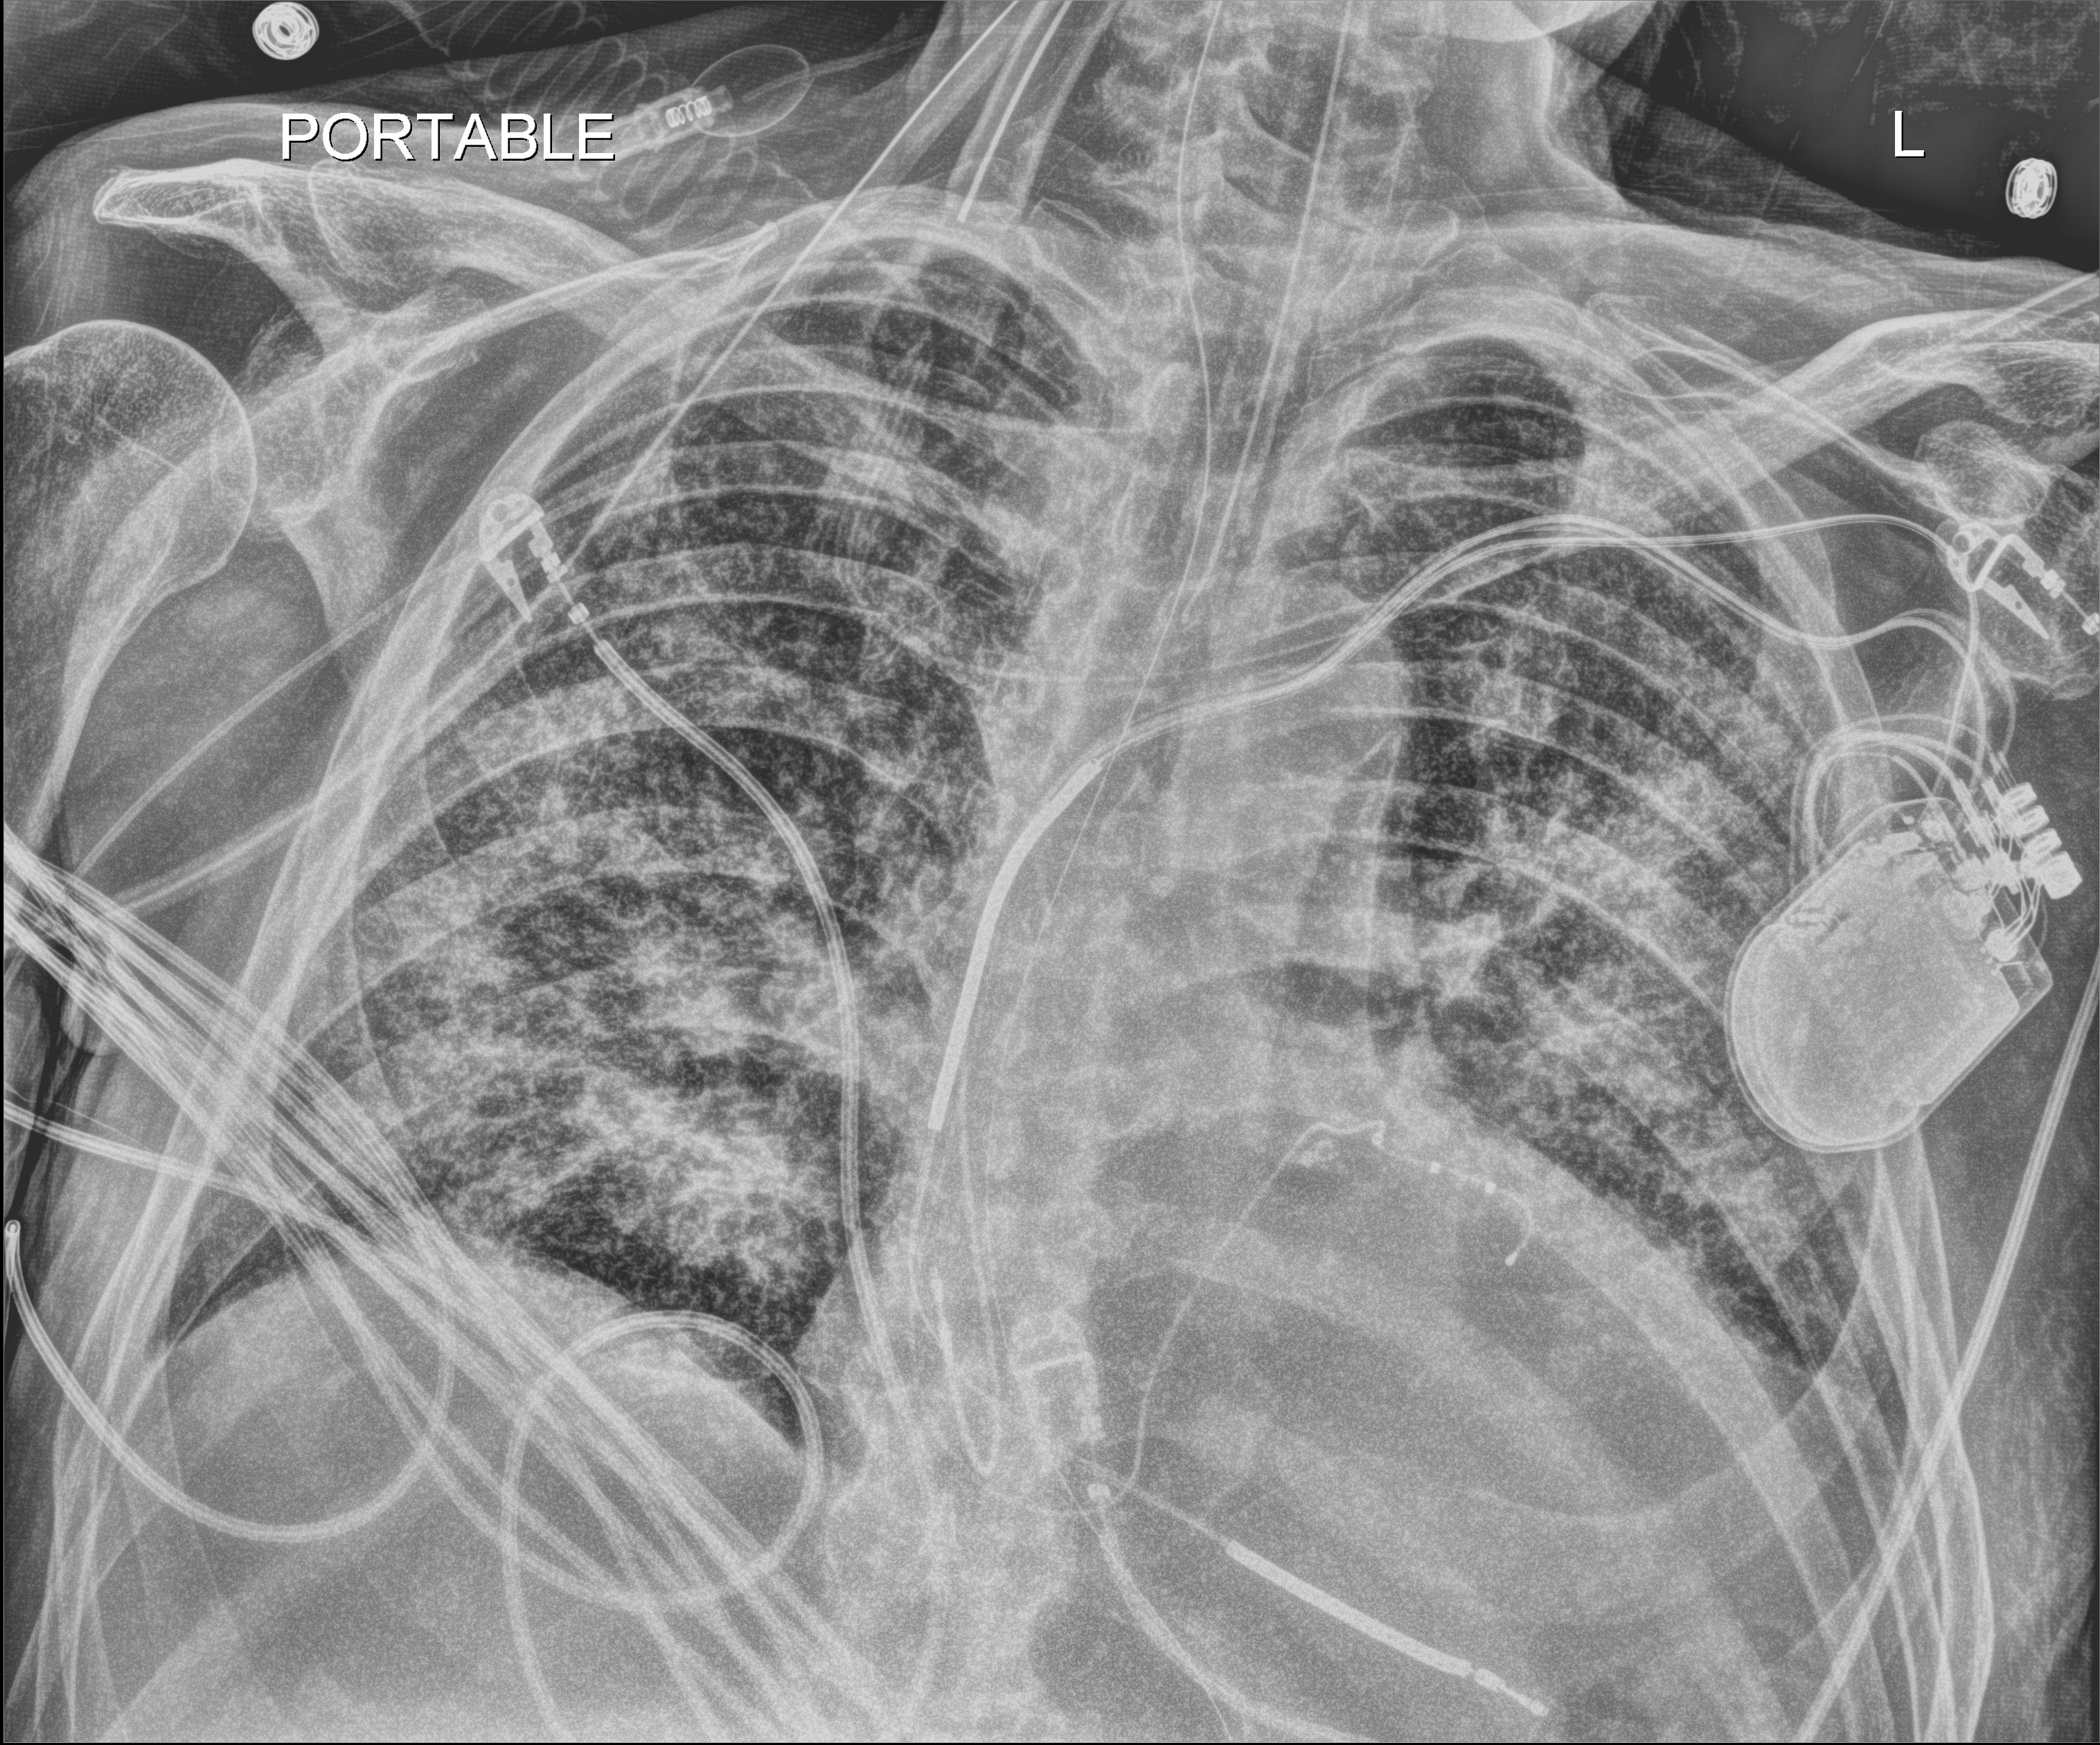
Chest X-ray (portable); anteroposterior (AP) projection. Patient hospitalised with COVID-19; male, aged 60–74 years.
Admission-level facts for this patient (not findings on this image; timing relative to this image not recorded): mechanically ventilated during this hospital stay: yes; diabetes (admission record): yes; admitted to intensive care during this hospital stay: yes.